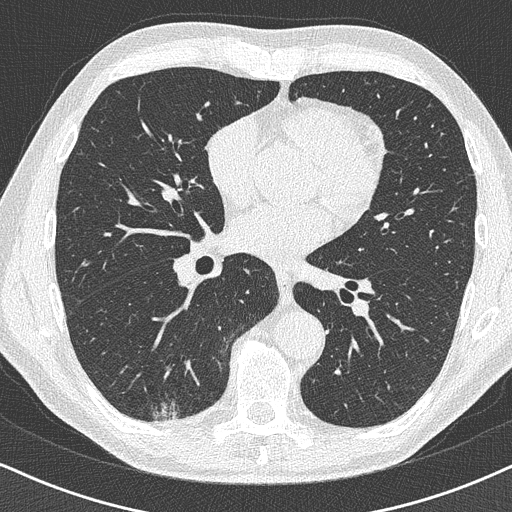
Axial slice from a low-dose chest CT screening exam; baseline screening round; lung window (W 1500 / L -600 HU); 1 mm slice thickness; lung (sharp) reconstruction kernel (B50f); slice 228 of 438 in the series; 512 × 512 image matrix. Male participant, aged 63 years at enrolment.
Expert-annotated lung lesion, bounding box <126,356,198,427> (left, top, right, bottom; pixels). Screening reader's record for this exam (one nodule recorded; not confirmed to be the boxed lesion): non-calcified nodule or mass ≥4 mm, right lower lobe, 16 × 13 mm, poorly defined margins. Later outcome: lung cancer diagnosed 74 days after this screen — adenocarcinoma, NOS, right lower lobe, moderately differentiated (G2), stage IA (AJCC 6th edition), 20 mm at pathology.